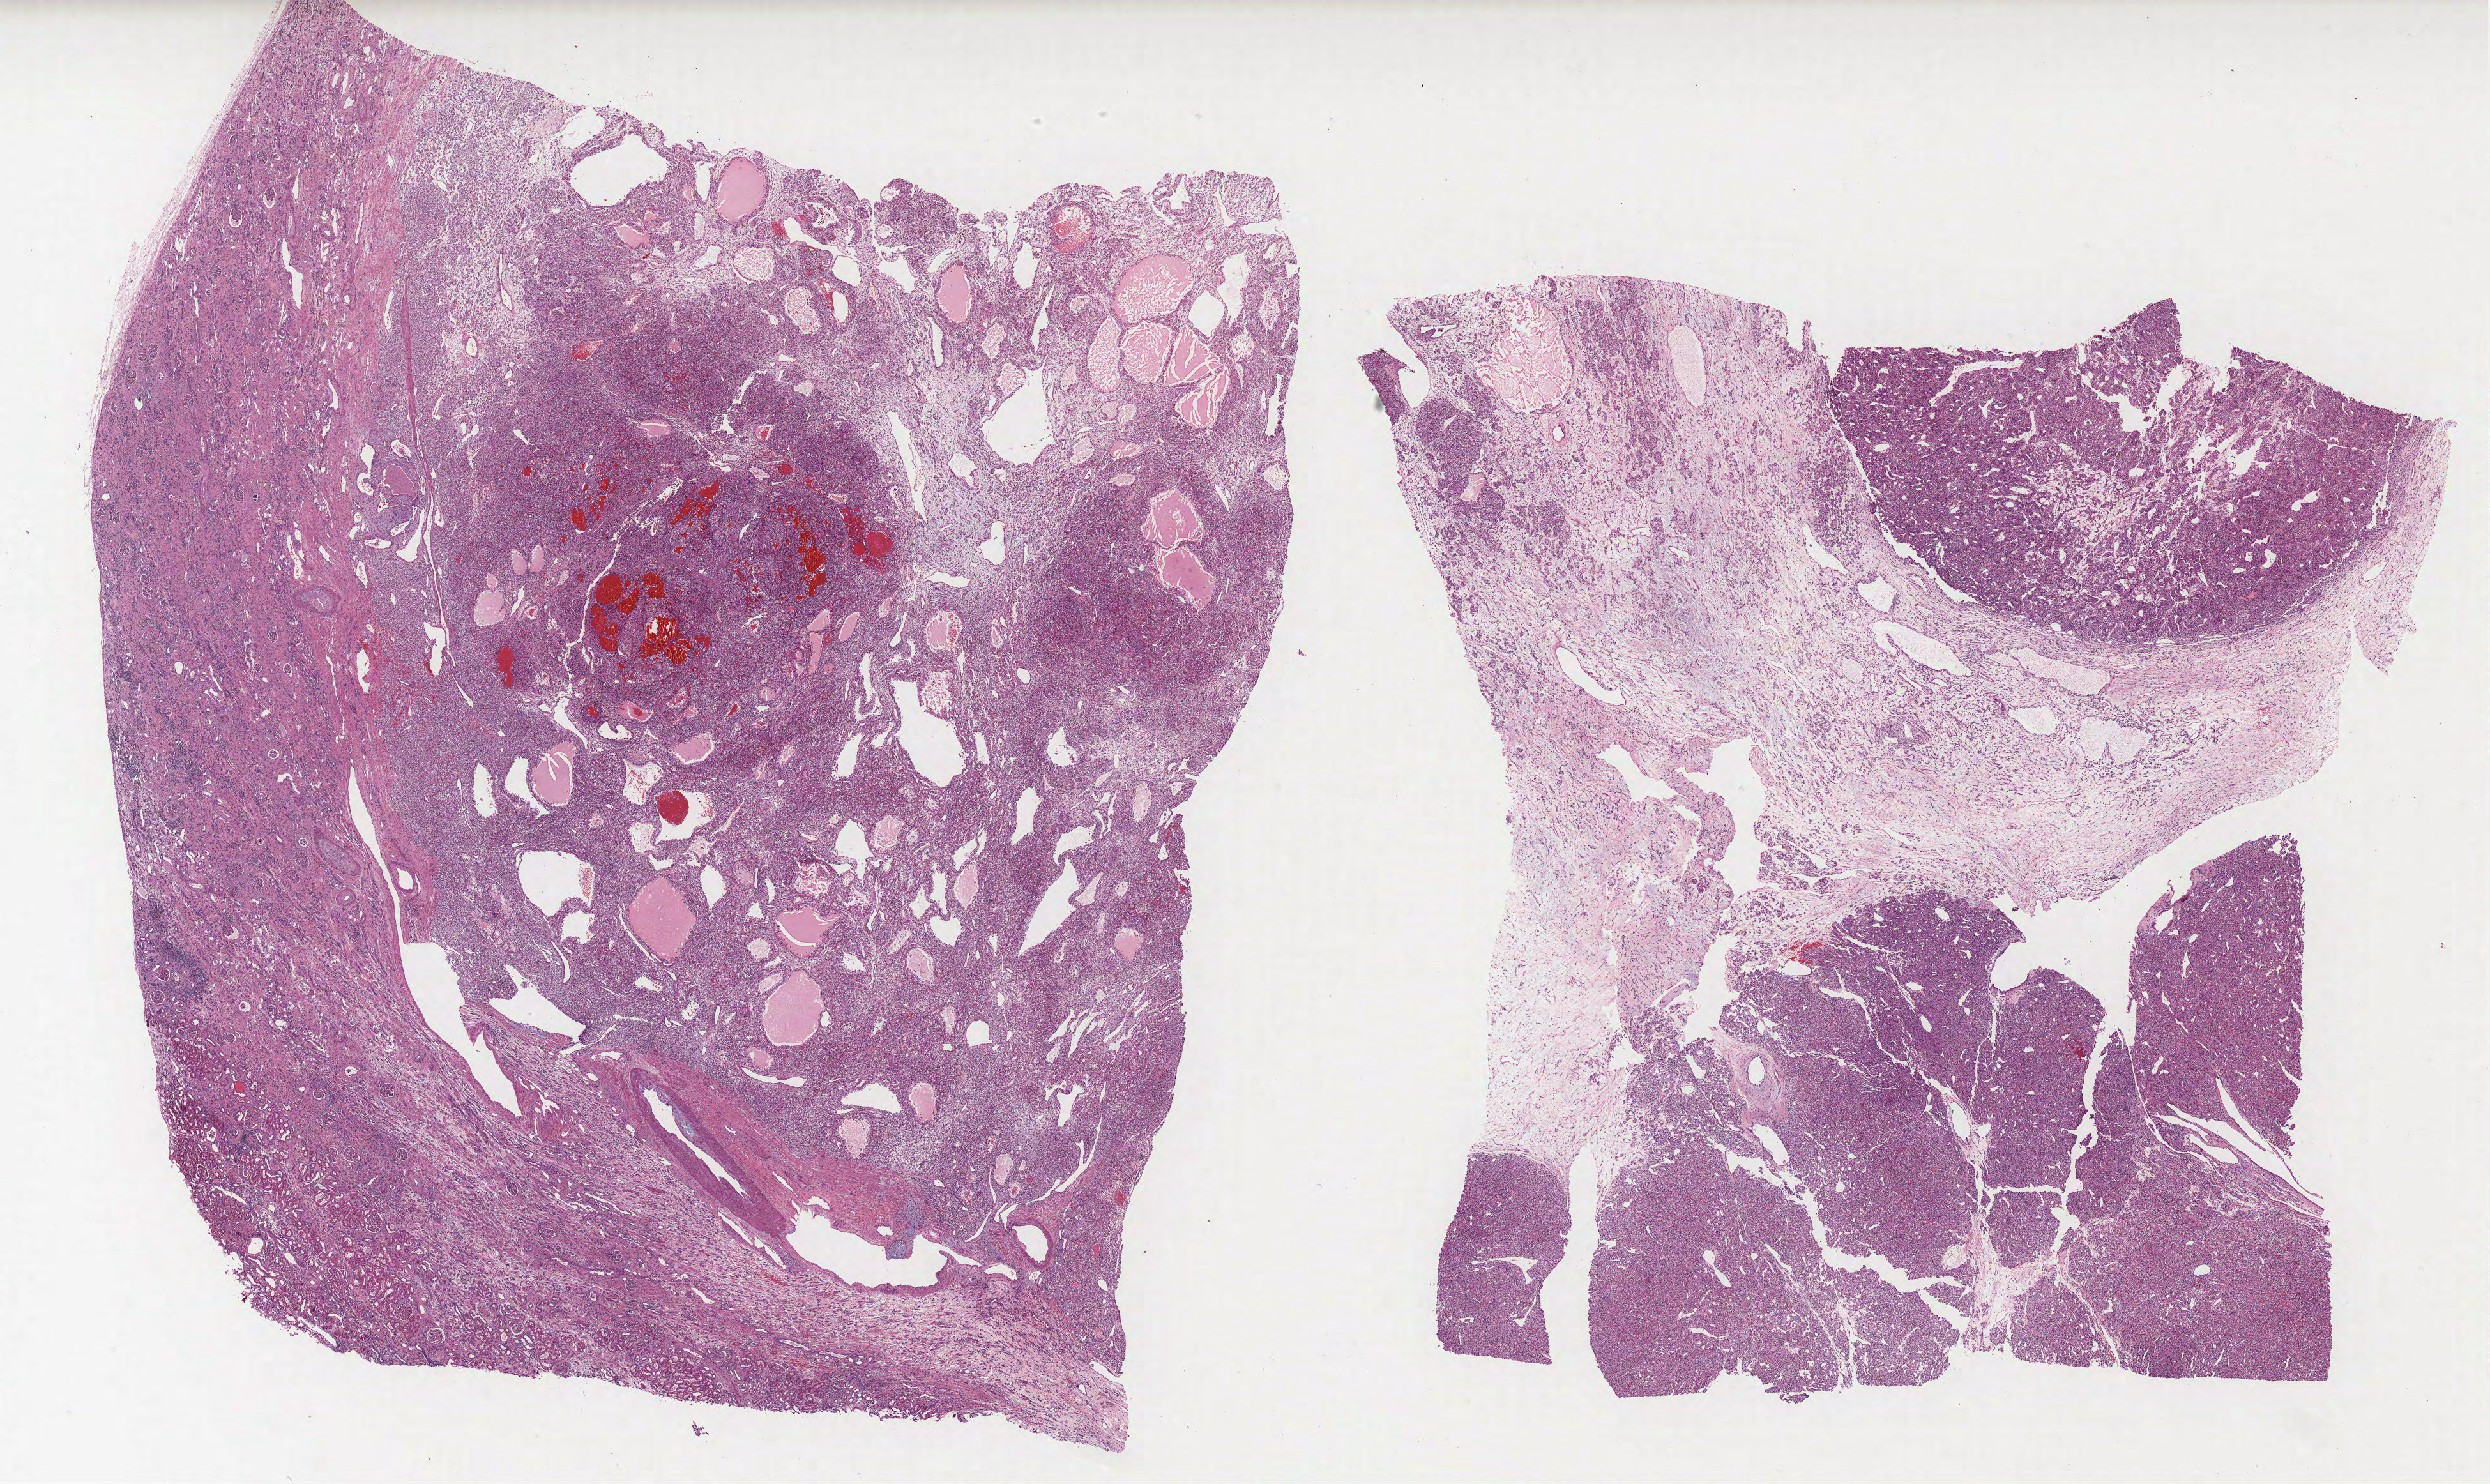
Whole-slide histology image, Hematoxylin and eosin (H&E) stained — shown as a low-resolution overview of the whole scanned area (about 31.2 x 18.6 mm, acquisition: 40x scan), formalin-fixed paraffin-embedded (FFPE) diagnostic section, kidney, primary tumour sample. Male, age 56 years at initial diagnosis. Histologic grade: G3 (poorly differentiated).
AJCC pathologic stage: I. TNM: T1a NX M0. Laterality: right. Diagnosis: Clear cell adenocarcinoma, NOS.